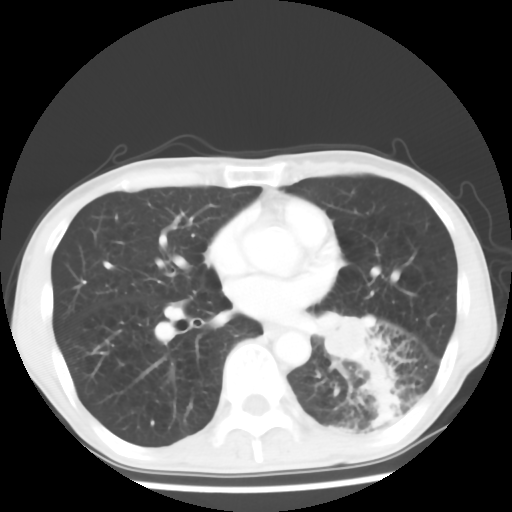
Chest CT, one axial slice; position 29 of 64 along the scan axis; reconstruction kernel STANDARD; 120 kVp; lung window (W 1500 / L -600 HU); 5 mm slice thickness; 512 × 512 image matrix, field of view 313 × 313 mm. Male patient, age 68 years. From the clinical record (not read from this slice): clinical TNM (as recorded): T4 N0 M0.
Structures marked on this image (rectangle marked by the reading radiologist):
- lung tumour (recorded histology: squamous cell carcinoma): bounding box [x1, y1, x2, y2] px = [311, 303, 375, 369]